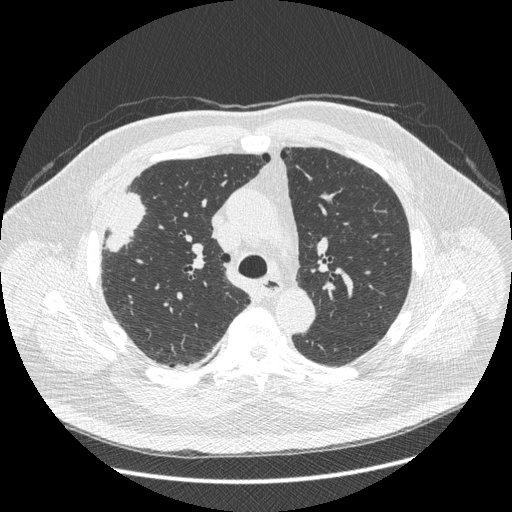
Axial slice from a low-dose chest CT screening exam, third annual screen, lung window (W 1500 / L -600 HU), standard (soft-tissue) reconstruction kernel (STANDARD), slice 136 of 426 in the series. Male participant, aged 66 years at enrolment.
Expert reader's lesion annotation, bounding box [x1, y1, x2, y2] px = [87, 193, 146, 267]. Screening reader's record for this exam (one nodule recorded; not confirmed to be the boxed lesion): non-calcified nodule or mass ≥4 mm, right upper lobe, 48 × 25 mm, spiculated (stellate) margins, soft tissue attenuation, pre-existing on the prior screen: no. Later outcome: lung cancer diagnosed 35 days after this screen — non-small cell carcinoma, right upper lobe, stage IV (AJCC 6th edition), 50 mm at pathology.